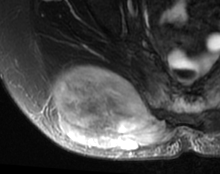
MRI of an extremity soft-tissue mass, one axial slice. Position 30 of 63 along the scan axis. T2-weighted fat-saturated. MR volume resampled by the dataset authors to the PET/CT grid (not the native acquisition matrix). 3.27 mm slice thickness. 220 × 174 image matrix, field of view 215 × 170 mm. Female patient. Case-level facts recorded for this patient, not image findings: histological type: spindle cell suggestive of myxofibrosarcoma; grade: intermediate; site of the primary tumour: right buttock.
Structures marked on this image (expert contour drawn on MRI and transferred to this co-registered scan by the dataset authors):
- gross tumour volume (mass): box from (x=52, y=66) to (x=176, y=153) px